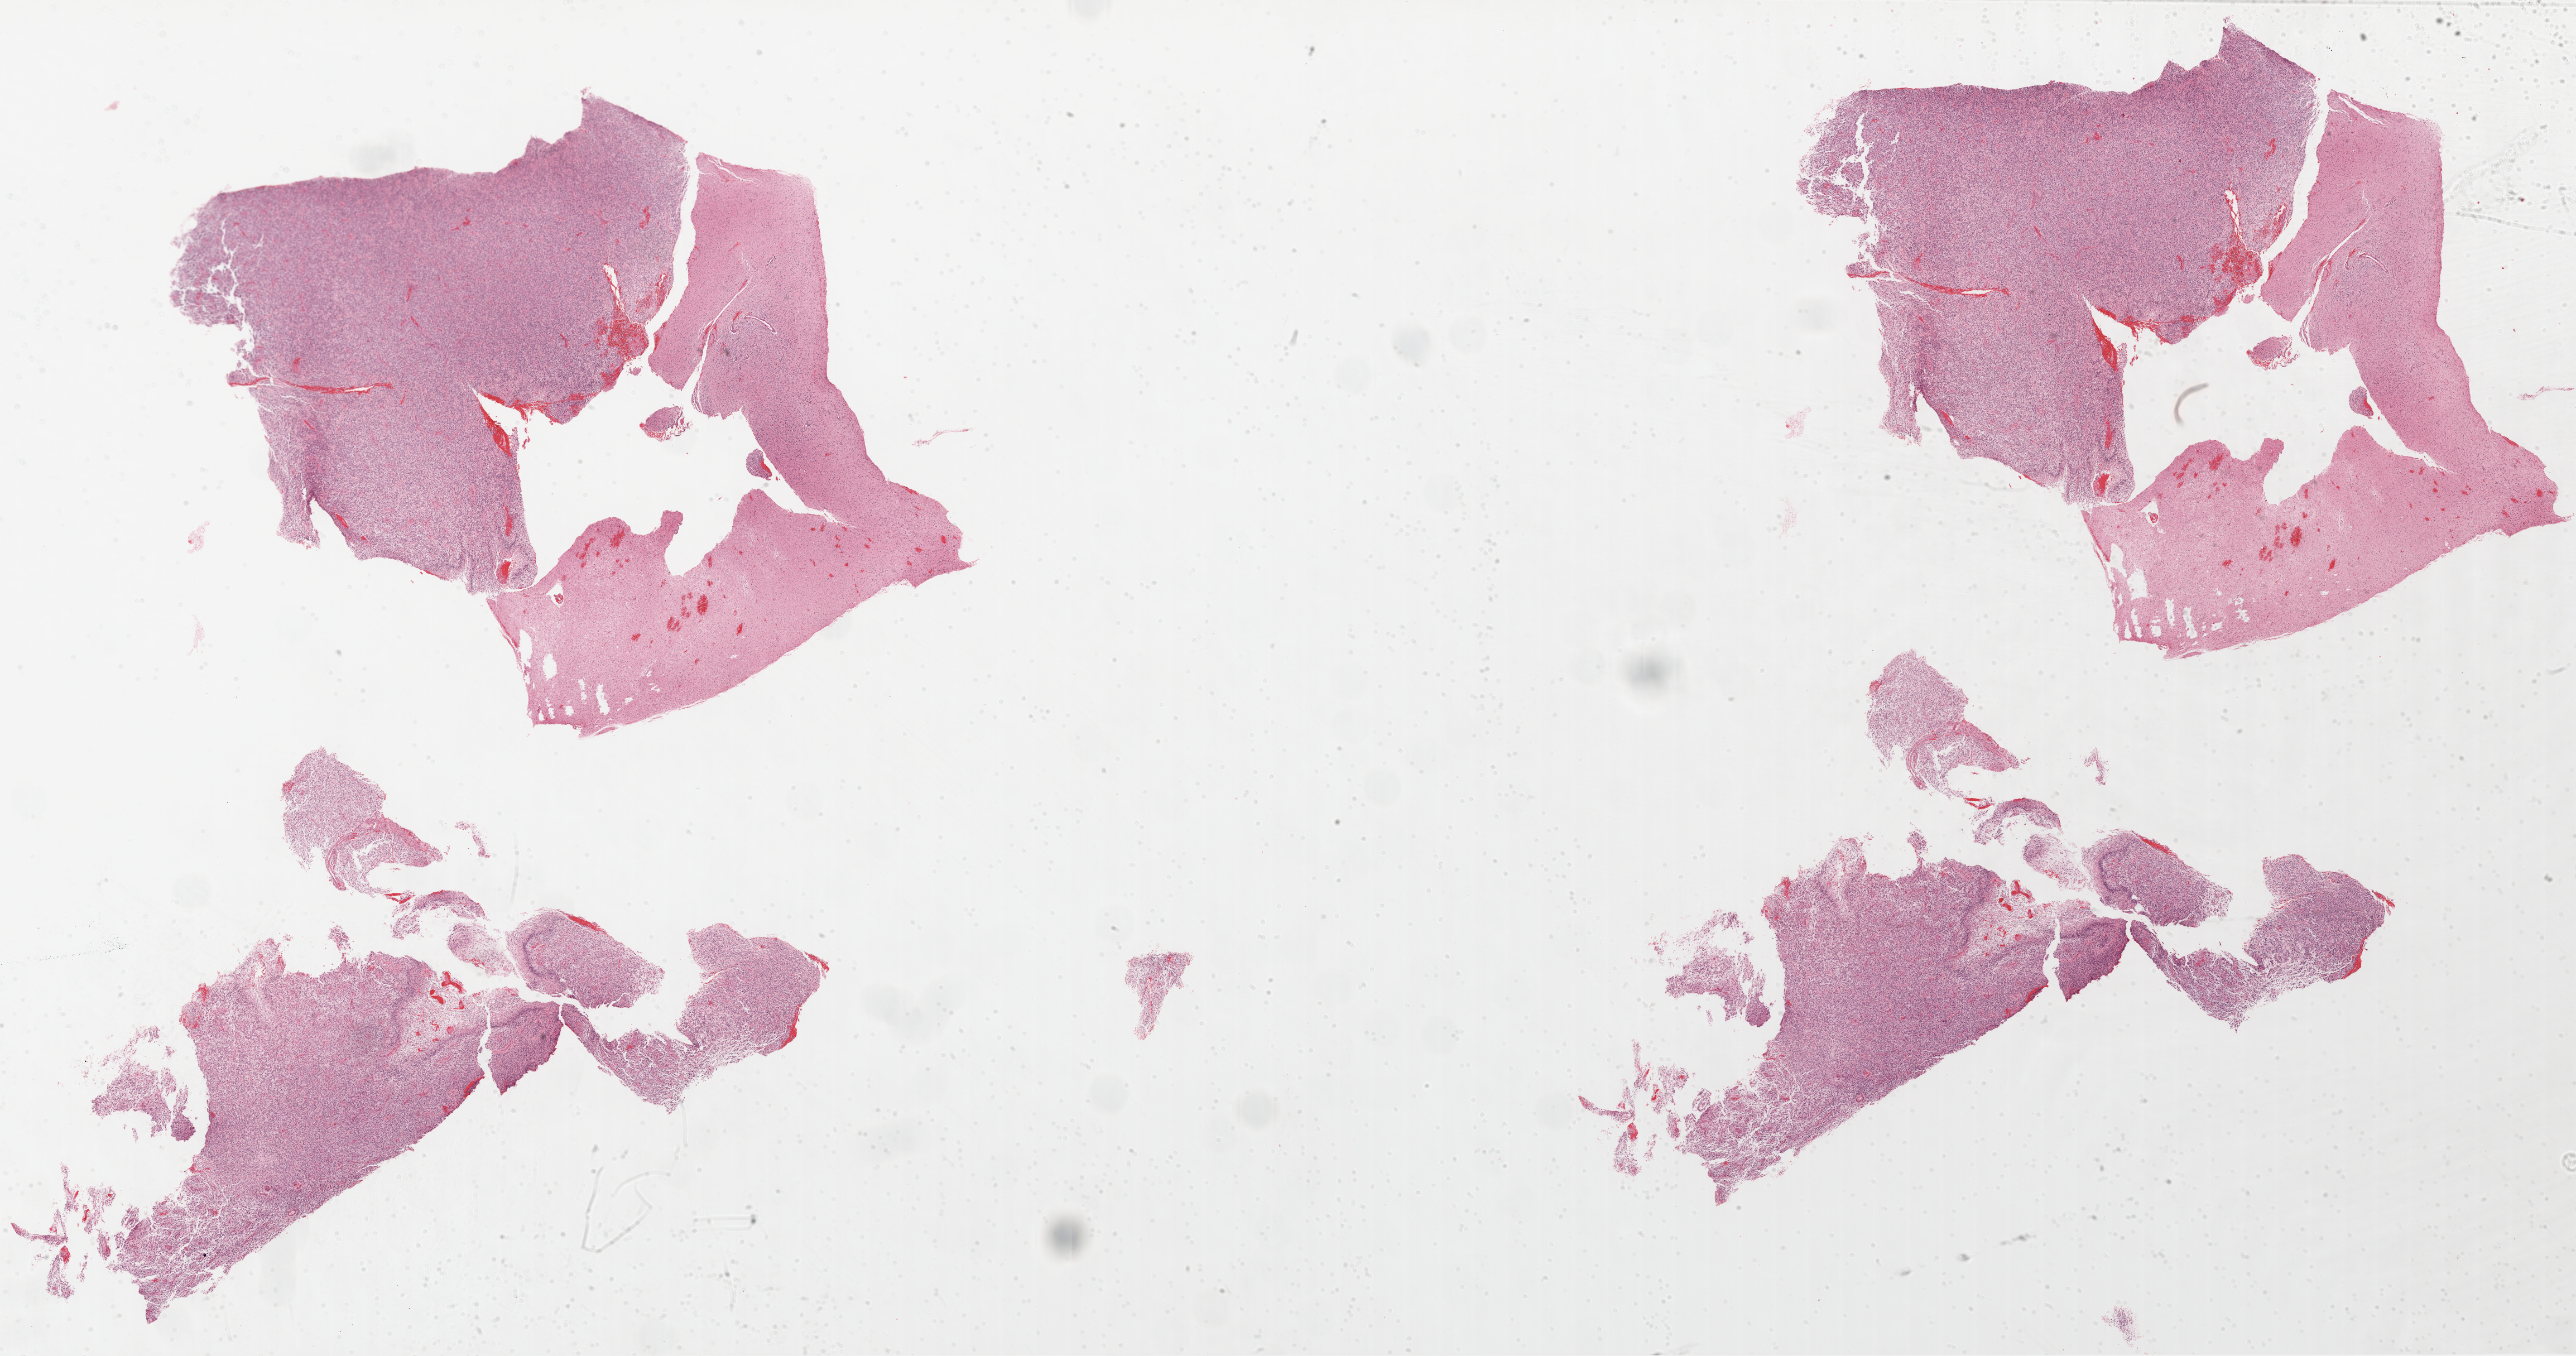
H&E-stained whole-slide image — shown as a low-resolution overview of the whole scanned area (about 37.2 x 19.6 mm, from a 20x scan). Formalin-fixed paraffin-embedded (FFPE) diagnostic section. Primary tumour sample from the brain. Male patient; age at initial diagnosis 65 years.
- histologic diagnosis: Glioblastoma